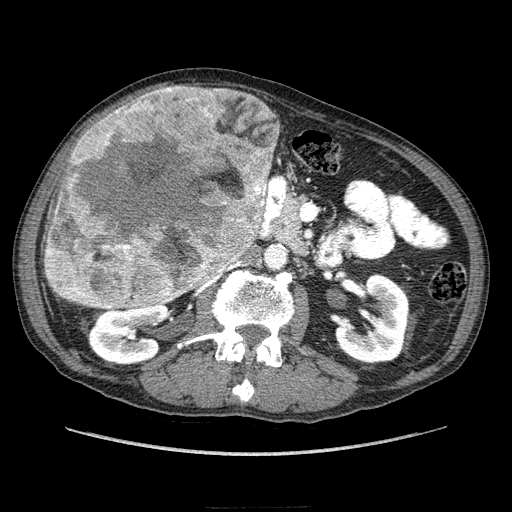
Contrast-enhanced abdominal CT (liver protocol), one axial slice; 100 kVp; soft-tissue window (W 400 / L 40 HU); 2.5 mm slice thickness; 512 × 512 image matrix, field of view 380 × 380 mm. From the clinical record (not read from this slice): diagnosis: hepatocellular carcinoma (patient treated with transarterial chemoembolisation; whether this scan precedes or follows treatment is not stated here); TNM stage (as recorded): Stage-IIIA; Child-Pugh class: A; tumour differentiation: well differentiated; tumour nodularity: multinodular.
Annotated regions visible in this slice (semi-automatic segmentation, software-assisted and operator-edited):
- liver parenchyma outside the tumour (the mass and vessels are separate outlines, so this box may not span the whole liver): box from (x=70, y=106) to (x=276, y=270) px
- mass: (x=40, y=86)–(x=276, y=312)
- liver vessels: (x=229, y=262)–(x=240, y=268)